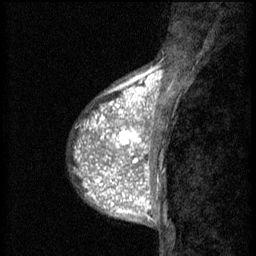
Breast MRI (dynamic contrast-enhanced), one sagittal slice; slice 20 of 60 in the series (ordered by position); 3 images stored at this slice position (order not interpretable as contrast timing); 1.5 T; TE 4.2 ms, TR 8.2 ms; 256 × 256 image matrix, field of view 180 × 180 mm. Patient: female, 38 years.
Structures marked on this image (semi-automatically segmented with operator editing):
- analysis volume of interest (the breast-tissue region the enhancement analysis was run in; not a lesion): bounding box [x1, y1, x2, y2] px = [92, 112, 152, 171]
- tumour enhancement mask (voxels above the 70 % enhancement threshold inside the analysis volume of interest): [92, 112, 152, 171]